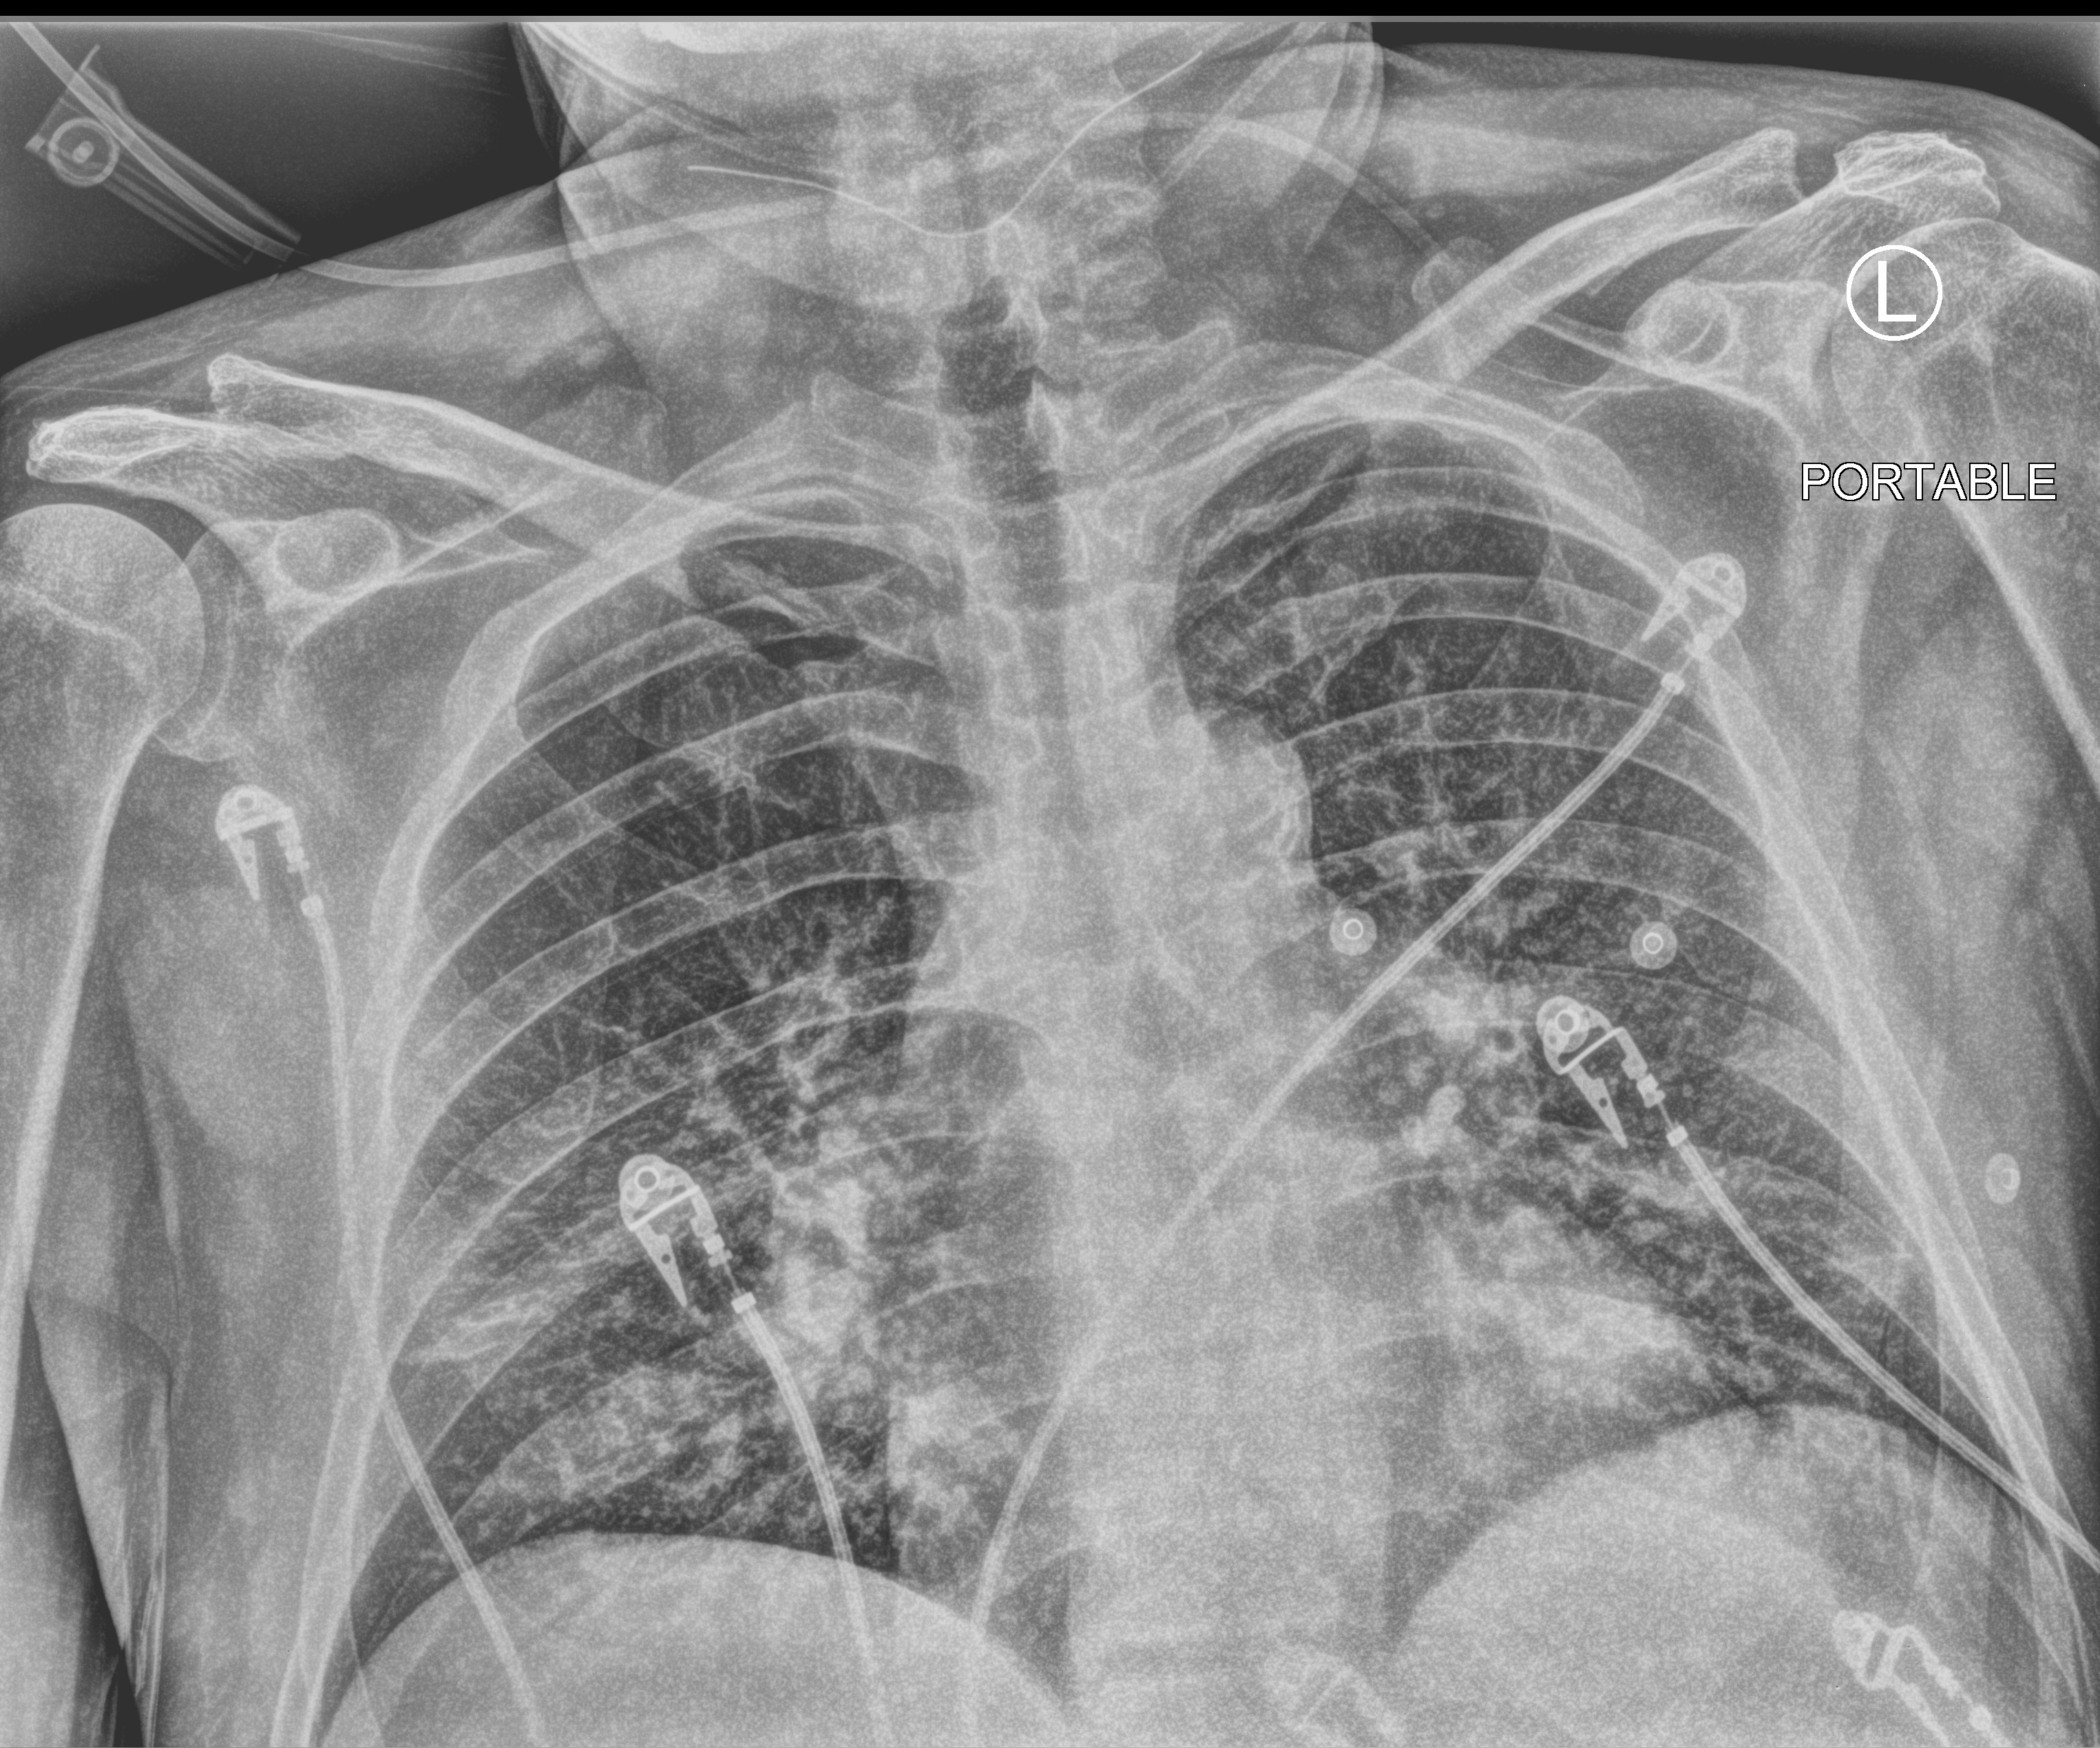
Portable chest radiograph. Patient hospitalised with COVID-19; male, aged 18–59 years.
From the hospital-stay record, not from the radiograph (when in the stay this image was taken is not recorded): mechanically ventilated during this hospital stay: no.